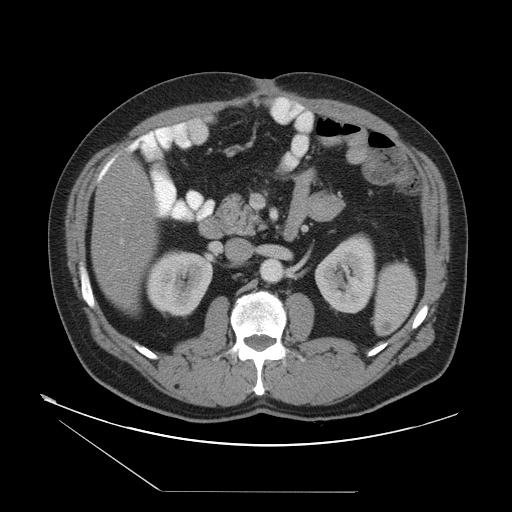
Contrast-enhanced abdominal CT, one axial slice; position 19 of 55 along the scan axis; intravenous contrast given; soft-tissue window (W 400 / L 40 HU); 5 mm slice thickness; 512 × 512 image matrix, field of view 454 × 454 mm. Male patient, age 59 years. Case-level facts recorded for this patient, not image findings: diagnosis: colorectal cancer liver metastases, imaged before liver resection; multiple liver metastases: yes; largest metastasis: 0.3 cm; disease in both lobes: yes.
Outlined on this slice (expert manual segmentation):
- hepatic veins: bounding box (x1, y1, x2, y2) in pixels: (121, 169, 138, 270)
- liver: (91, 160, 157, 309)
- planned liver remnant (the part of the liver to remain after resection): (91, 160, 157, 308)
- portal vein (with intrahepatic branches): (120, 203, 130, 244)